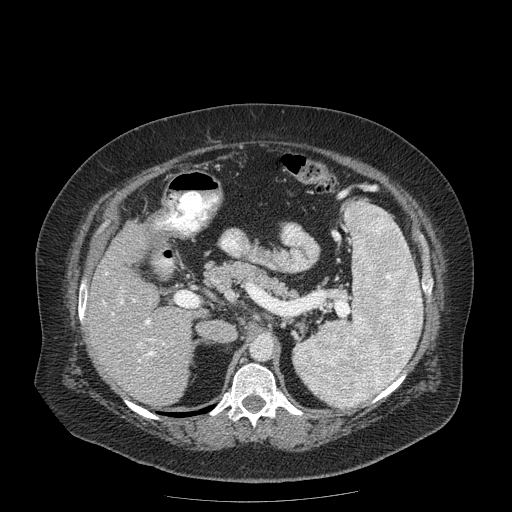
Contrast-enhanced abdominal CT (liver protocol), one axial slice; 120 kVp; soft-tissue window (W 400 / L 40 HU); 512 × 512 image matrix, field of view 440 × 440 mm. Case-level facts recorded for this patient, not image findings: diagnosis: hepatocellular carcinoma (patient treated with transarterial chemoembolisation; whether this scan precedes or follows treatment is not stated here); TNM stage (as recorded): Stage-IIIB; Child-Pugh class: A; tumour differentiation: well differentiated; tumour nodularity: uninodular.
Structures marked on this image (semi-automatically segmented with operator editing):
- liver parenchyma outside the tumour (the mass and vessels are separate outlines, so this box may not span the whole liver): box from (x=88, y=222) to (x=199, y=408) px
- liver vessels: (x=103, y=272)–(x=164, y=370)